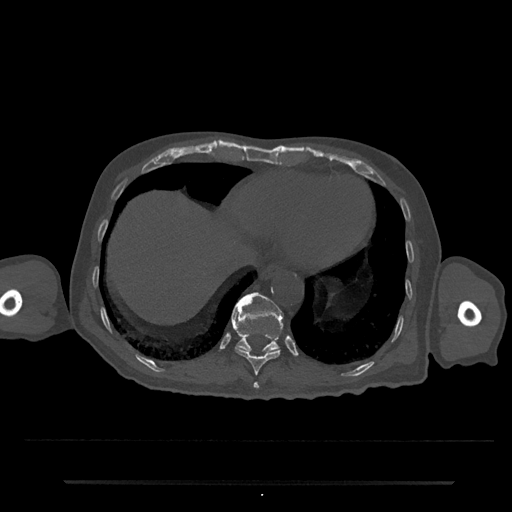
CT including the spine, one axial slice. Slice 292 of 797 in the series (ordered by position). Reconstruction kernel Br40s/3. 120 kVp. Bone window (W 1800 / L 400 HU). 0.5 mm slice thickness. 512 × 512 image matrix, field of view 427 × 427 mm. Patient: male, 74 years. From the clinical record (not read from this slice): primary cancer: prostate.
Annotated regions visible in this slice (semi-automatically segmented with operator editing):
- T10 vertebra: bounding box [x1, y1, x2, y2] px = [231, 315, 282, 376]
- T11 vertebra: [232, 292, 284, 353]
- T9 vertebra: [253, 382, 259, 389]